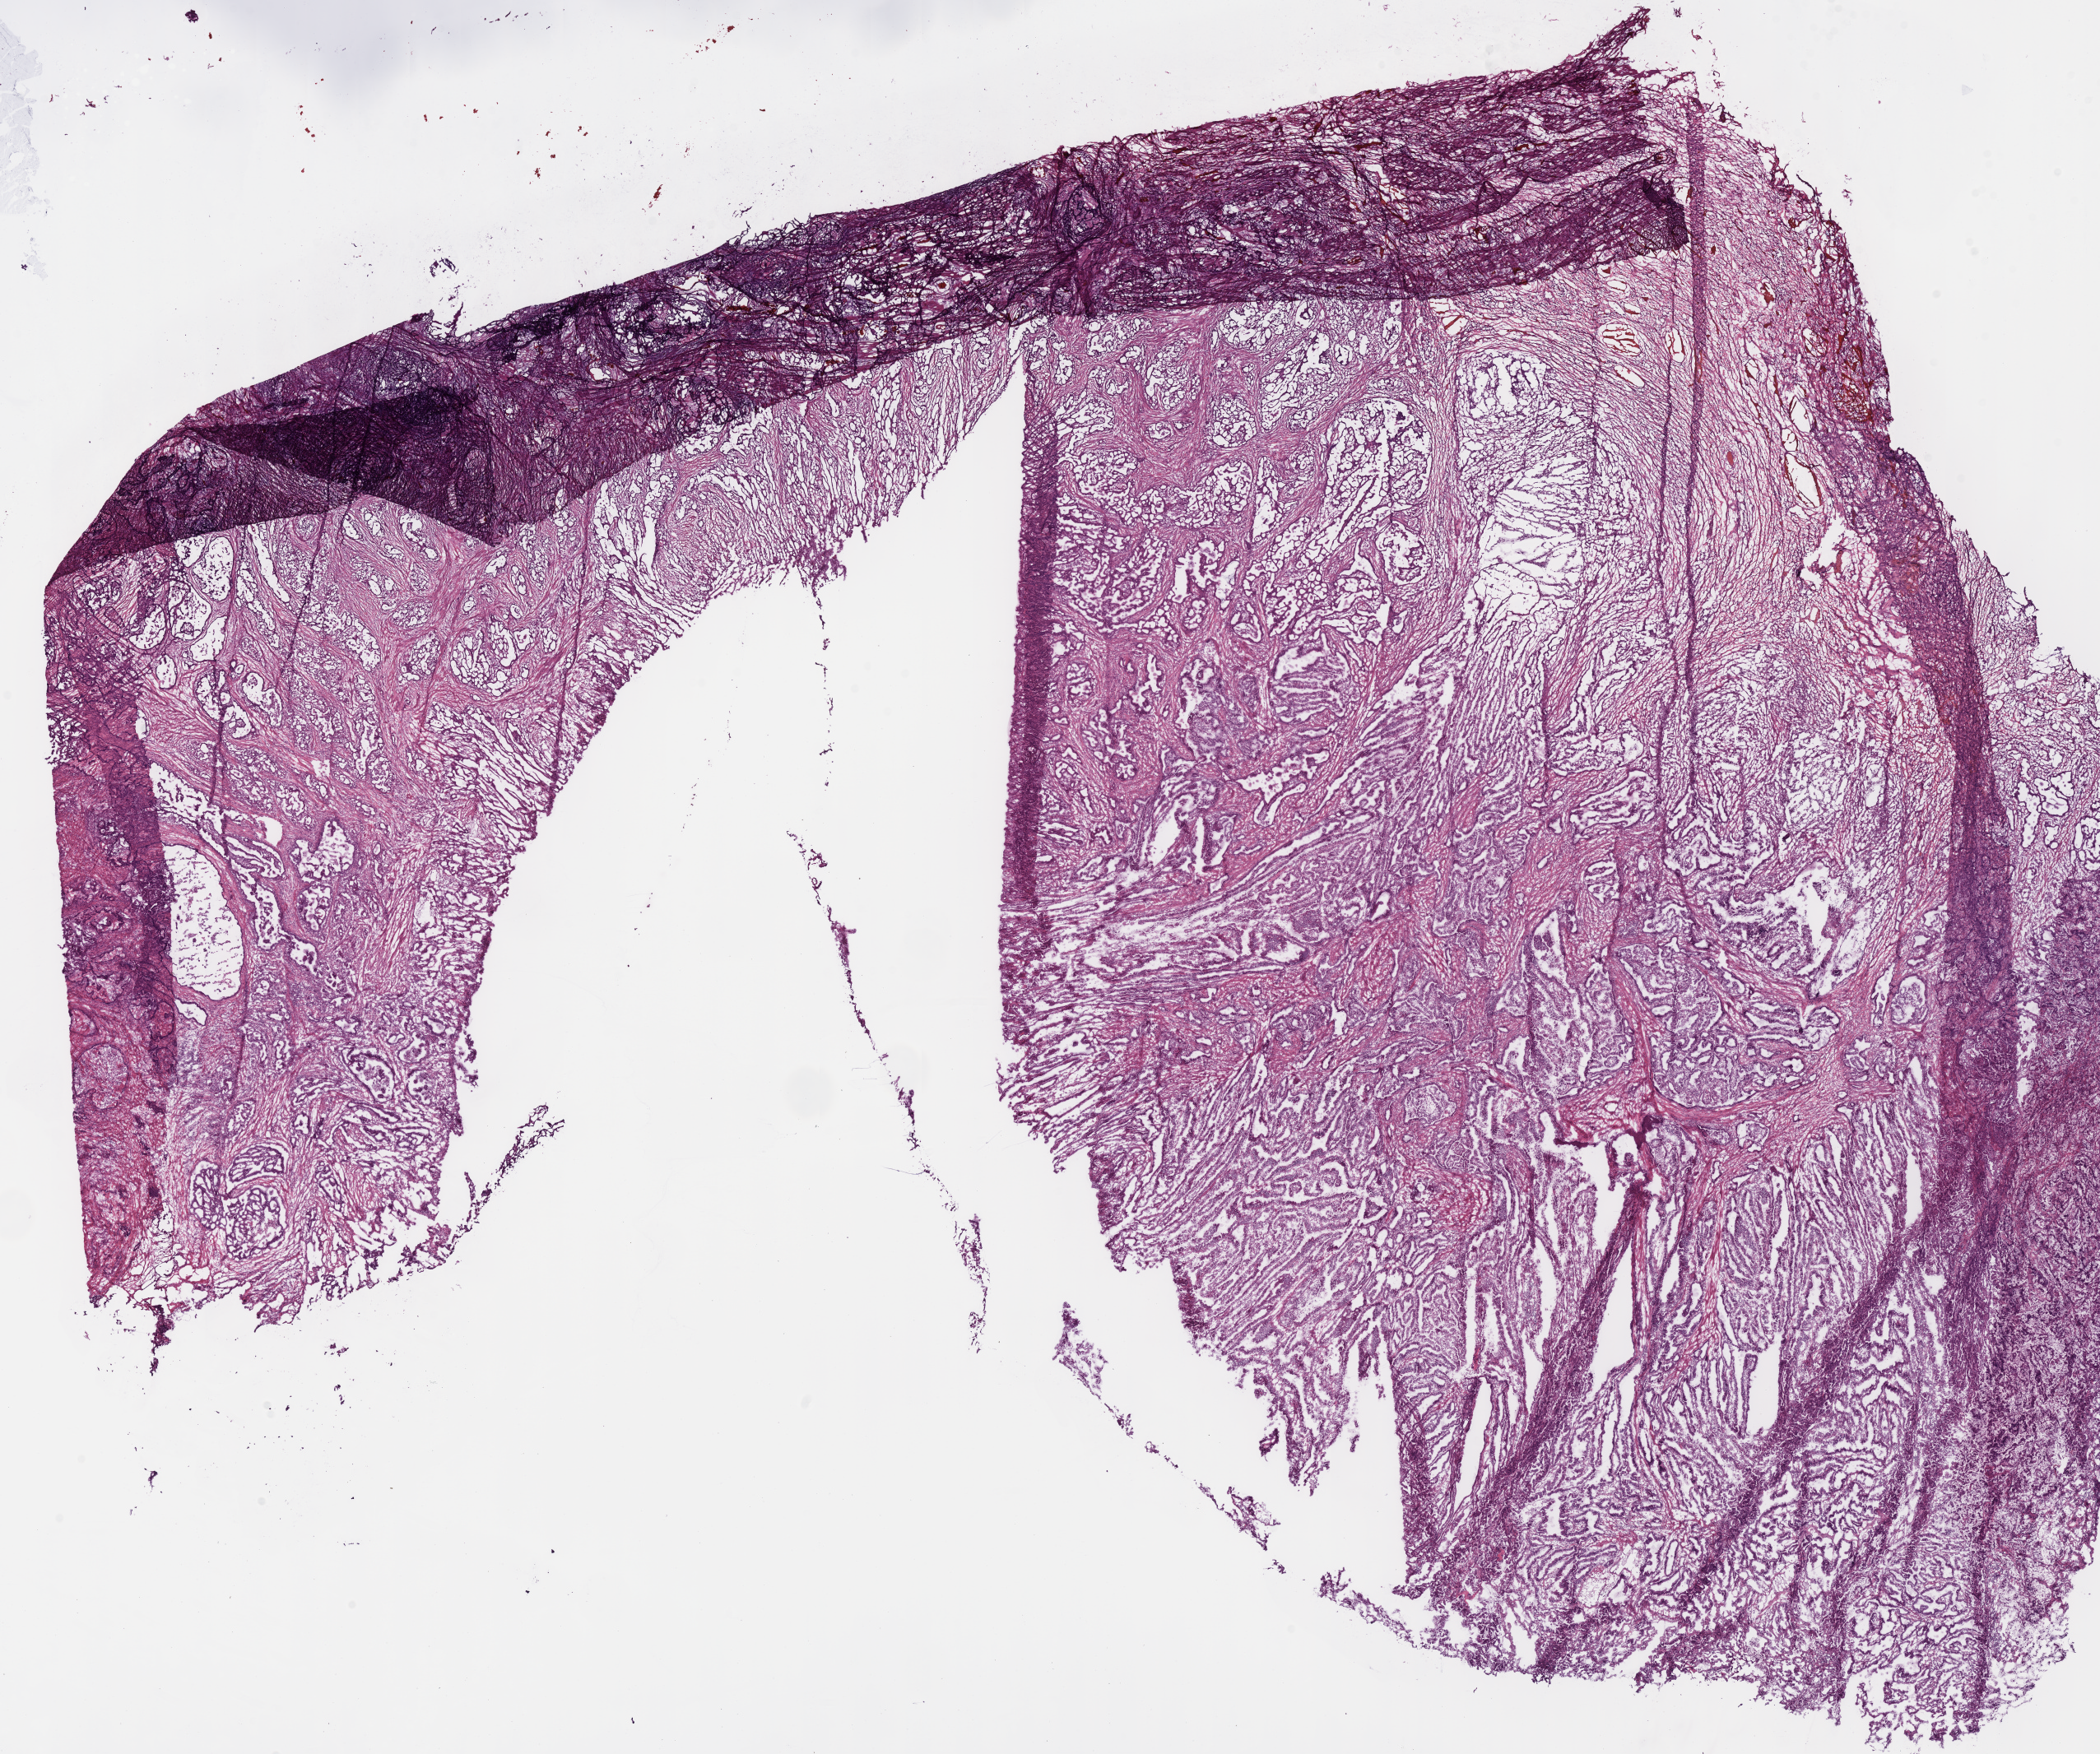
Hematoxylin and eosin (H&E) stained whole-slide image, whole scanned area (about 20.1 x 16.8 mm) shown as a low-resolution overview. Frozen section from the top of the tissue portion. Stomach, primary tumour sample. Male, age 49 years at initial diagnosis. Histologic grade: G3 (poorly differentiated). Composition of this section per pathologist review: tumour cells 82%, tumour nuclei 85%, normal cells 0%, stromal cells 15%, necrosis 3%.
AJCC pathologic stage: II (7th edition). Pathologic diagnosis: Adenocarcinoma, intestinal type (gastric antrum).